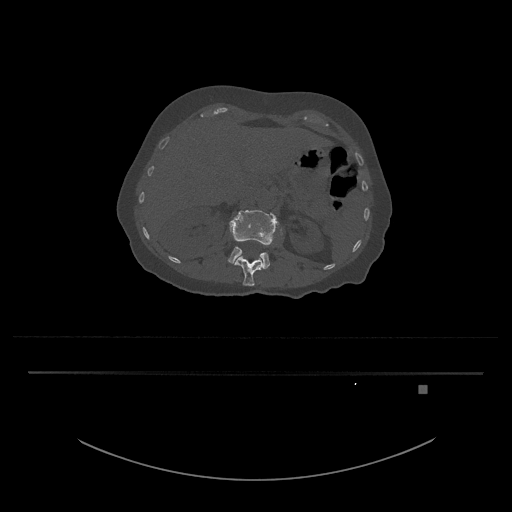
CT including the spine, one axial slice; slice 524 of 797 in the series (ordered by position); reconstruction kernel Br40s/3; bone window (W 1800 / L 400 HU); 512 × 512 image matrix, field of view 500 × 500 mm. Patient: female, 57 years. Case-level facts recorded for this patient, not image findings: primary cancer: cervical.
Structures marked on this image (semi-automatic segmentation, software-assisted and operator-edited):
- L1 vertebra: bounding box [x1, y1, x2, y2] px = [234, 229, 283, 286]